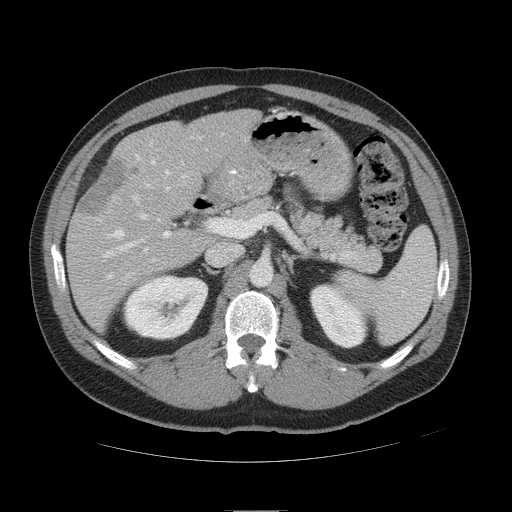
Contrast-enhanced abdominal CT, one axial slice. Position 27 of 49 along the scan axis. Reconstruction kernel STANDARD. 120 kVp. Soft-tissue window (W 400 / L 40 HU). 5 mm slice thickness. 512 × 512 image matrix, field of view 425 × 425 mm. Male patient, age 52 years. From the clinical record (not read from this slice): diagnosis: colorectal cancer liver metastases, imaged before liver resection; multiple liver metastases: yes; largest metastasis: 5.1 cm; disease in both lobes: yes.
Structures marked on this image (outlined manually by an expert reader):
- hepatic veins: bounding box [x1, y1, x2, y2] px = [108, 136, 202, 279]
- liver: [69, 110, 256, 327]
- planned liver remnant (the part of the liver to remain after resection): [132, 110, 255, 197]
- portal vein (with intrahepatic branches): [102, 175, 212, 281]
- liver metastasis: [82, 160, 139, 218]